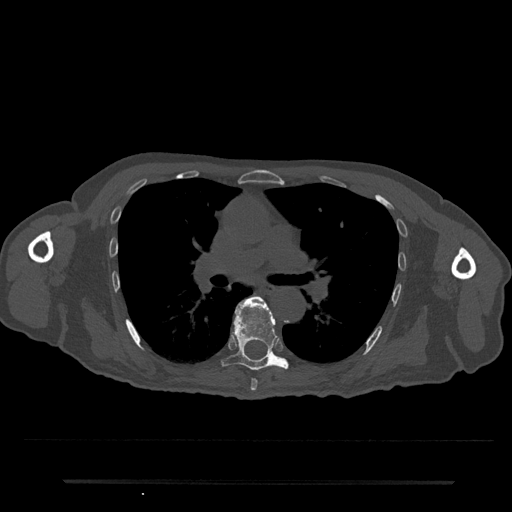
CT including the spine, one axial slice; reconstruction kernel Br40s/3; bone window (W 1800 / L 400 HU); 0.5 mm slice thickness; 512 × 512 image matrix. Male patient, age 74 years. From the clinical record (not read from this slice): primary cancer: prostate.
Structures marked on this image (semi-automatic segmentation, software-assisted and operator-edited):
- T6 vertebra: box from (x=250, y=378) to (x=258, y=391) px
- T7 vertebra: (x=220, y=298)–(x=289, y=371)